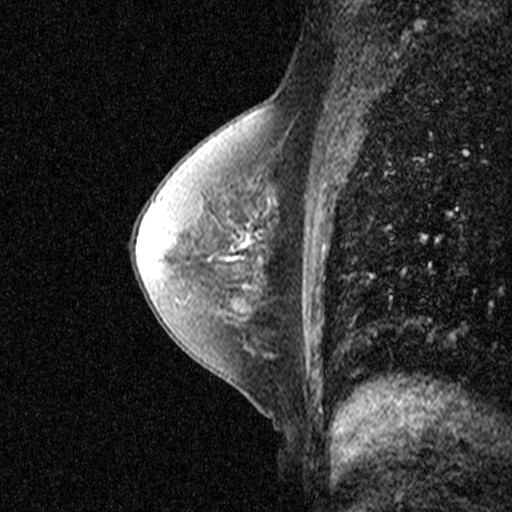
Breast MRI (dynamic contrast-enhanced), one sagittal slice; slice 22 of 40 in the series (ordered by position); dynamic contrast-enhanced study with each time point stored as its own series, time point 2 of 3 at this slice position (early post-contrast, ordered by acquisition time); 1.5 T; TE 4.5 ms, TR 11 ms; 3 mm slice thickness; 512 × 512 image matrix, field of view 200 × 200 mm. Female patient, age 55 years. Case-level facts recorded for this patient, not image findings: setting: breast cancer imaged before/during neoadjuvant chemotherapy; receptor status: HR-positive, HER2-negative.
Outlined on this slice (semi-automatic segmentation, software-assisted and operator-edited):
- analysis volume of interest (the breast-tissue region the enhancement analysis was run in; not a lesion): box from (x=194, y=202) to (x=279, y=277) px
- tumour enhancement mask (voxels above the 90 % enhancement threshold inside the analysis volume of interest): (x=243, y=243)–(x=246, y=246)